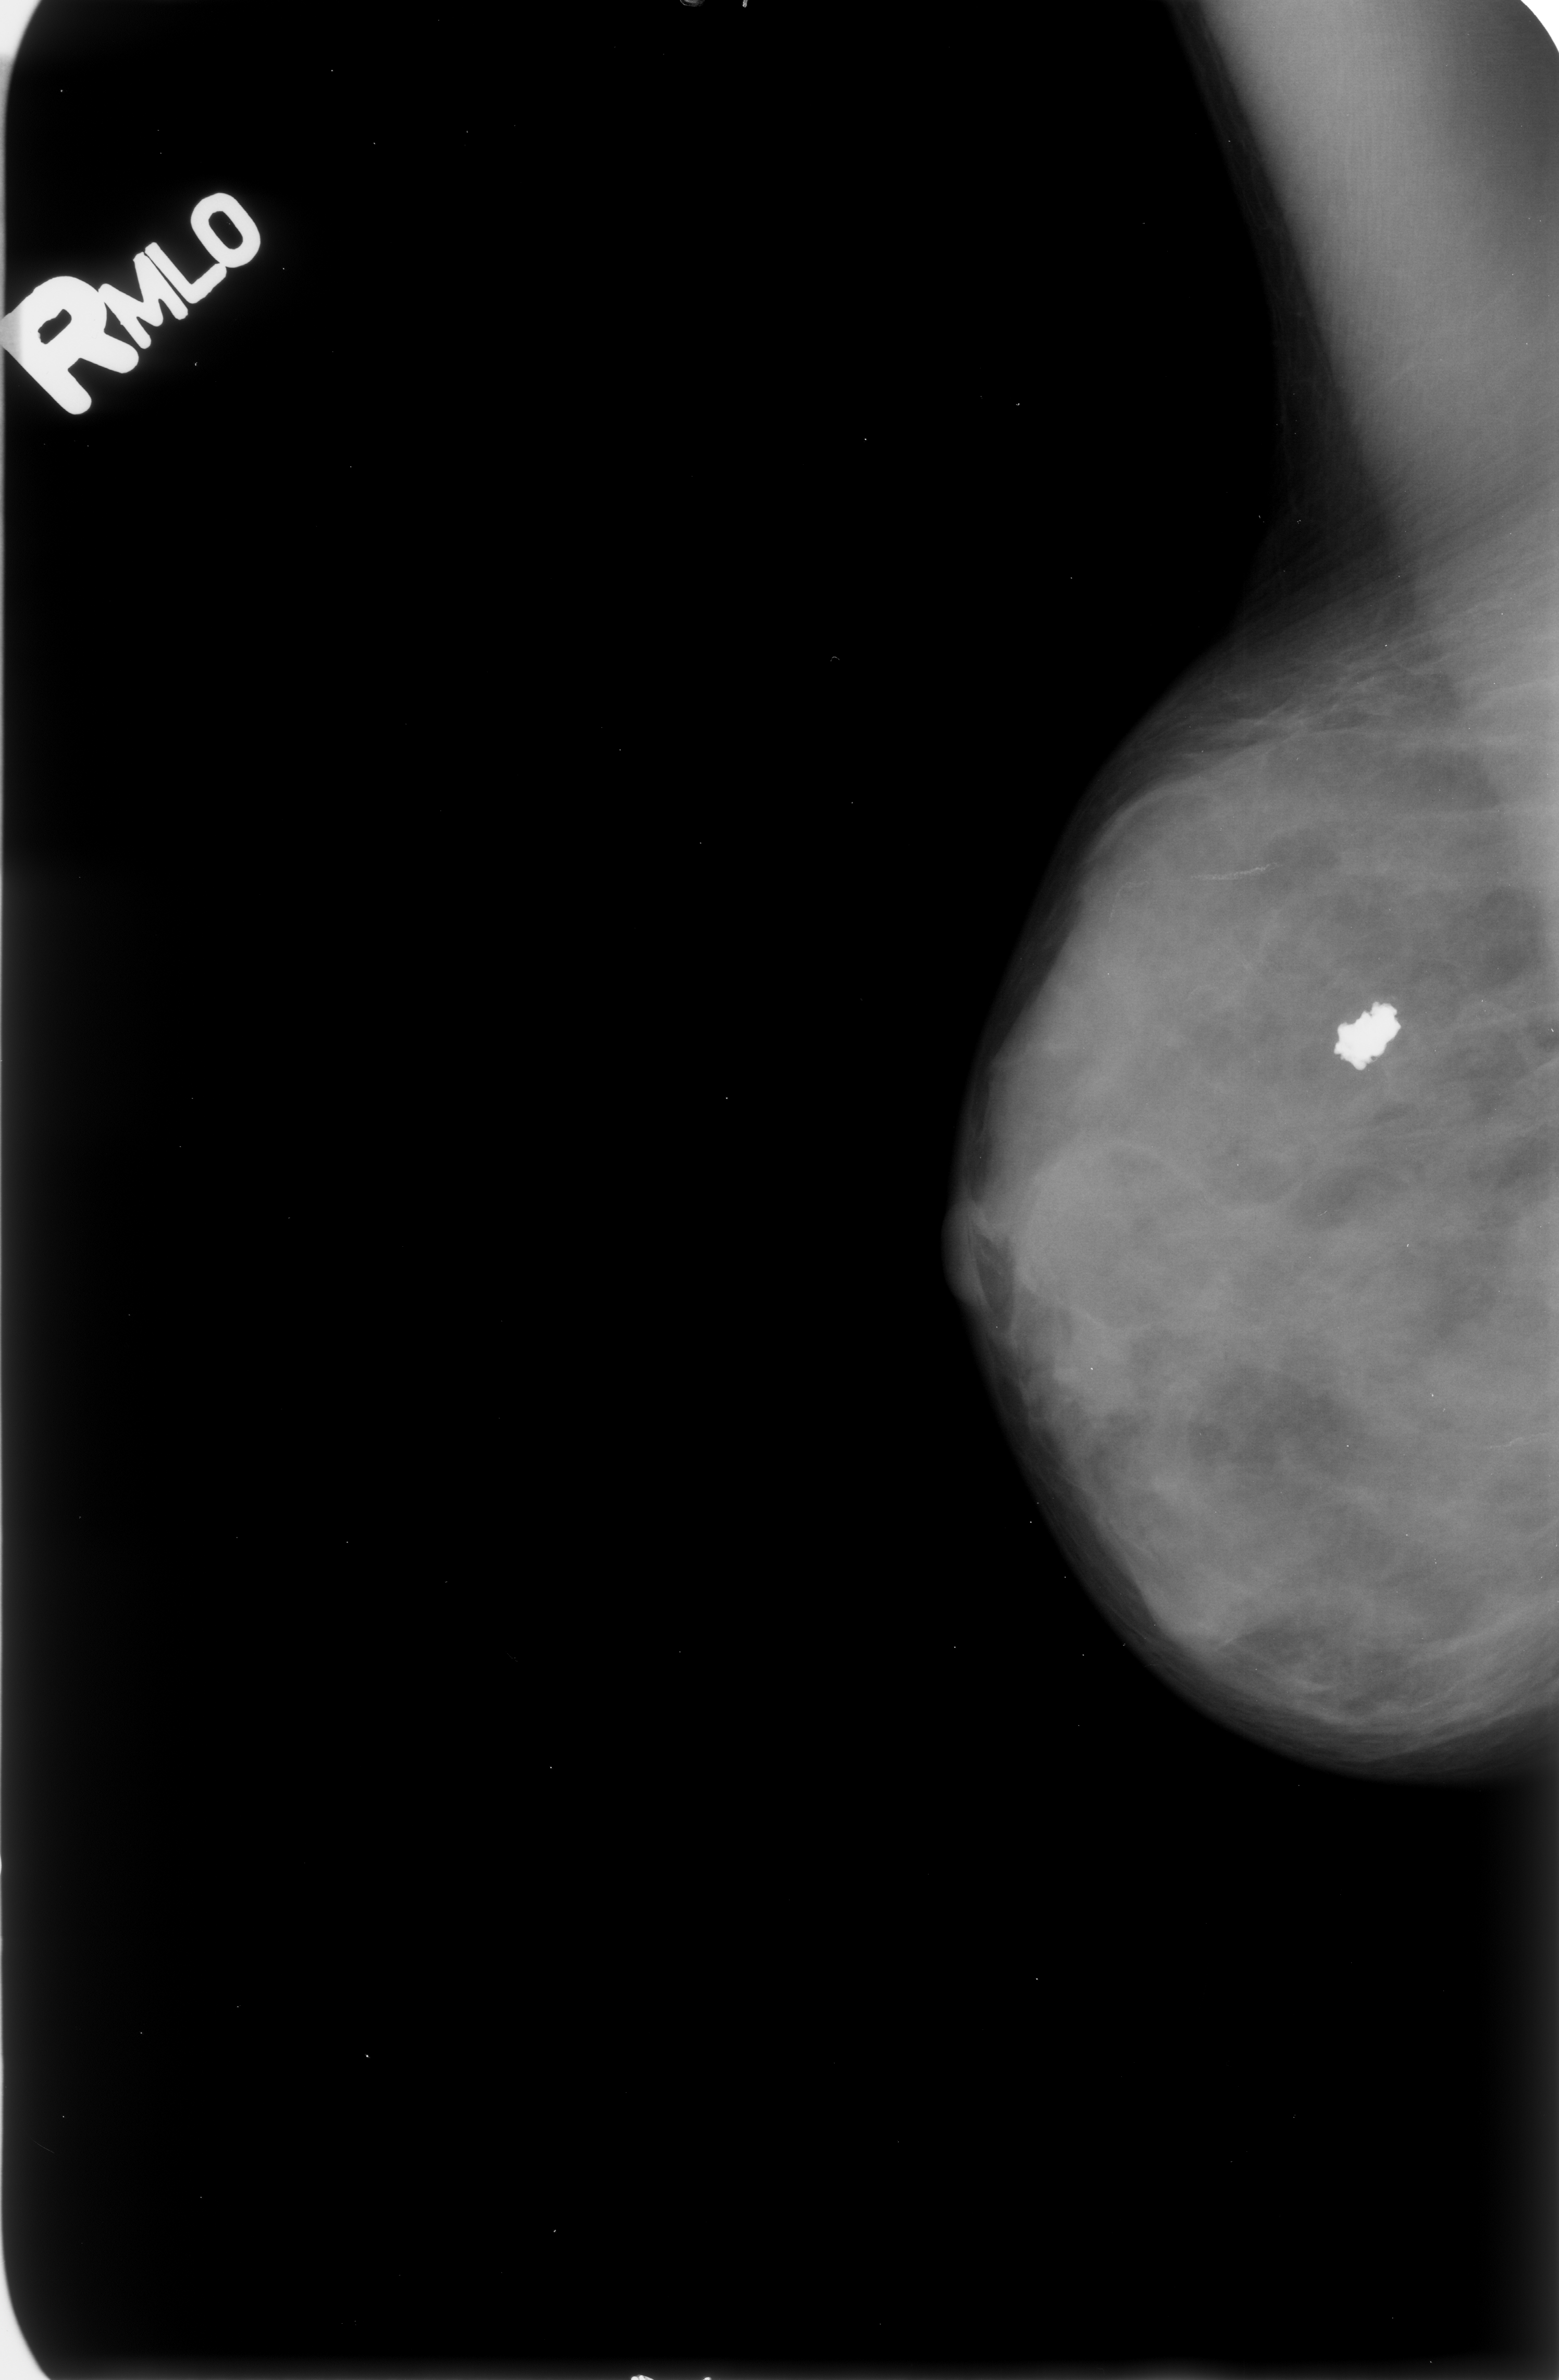
Mammogram (digitized film), right breast, MLO view, breast composition: extremely dense (BI-RADS density category 4 of 4).
Finding: calcifications, morphology coarse; BI-RADS assessment category 2; benign; no additional work-up was recommended (benign without callback).